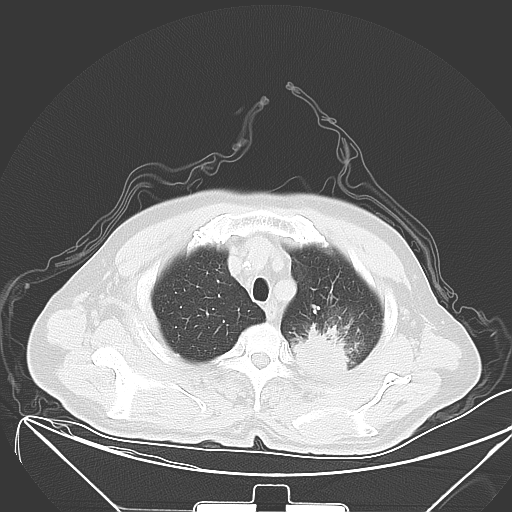
Chest CT, one axial slice; position 50 of 64 along the scan axis; 120 kVp; lung window (W 1500 / L -600 HU); 5 mm slice thickness; 512 × 512 image matrix, field of view 431 × 431 mm. Patient: male, 58 years. Case-level facts recorded for this patient, not image findings: clinical TNM (as recorded): T2b N3 M1b; histopathological grade: G3.
Outlined on this slice (rectangle marked by the reading radiologist):
- lung tumour (recorded histology: adenocarcinoma): bounding box (x1, y1, x2, y2) in pixels: (288, 313, 351, 380)